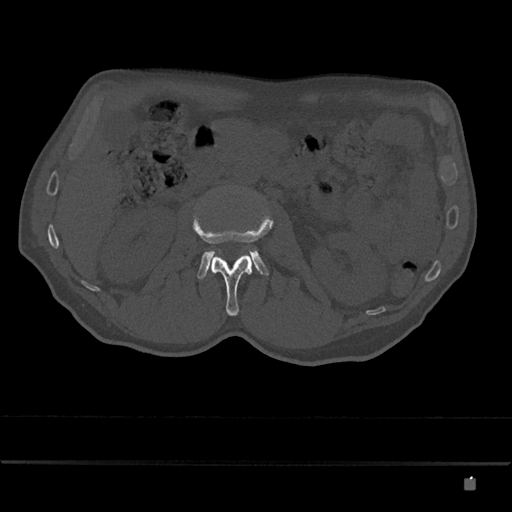
CT including the spine, one axial slice; position 454 of 797 along the scan axis; bone window (W 1800 / L 400 HU); 0.5 mm slice thickness; 512 × 512 image matrix. Patient: male, 72 years. From the clinical record (not read from this slice): primary cancer: prostate.
Annotated regions visible in this slice (semi-automatically segmented with operator editing):
- L2 vertebra: bounding box <193,214,274,316> (left, top, right, bottom; pixels)
- L3 vertebra: <197,227,269,279>